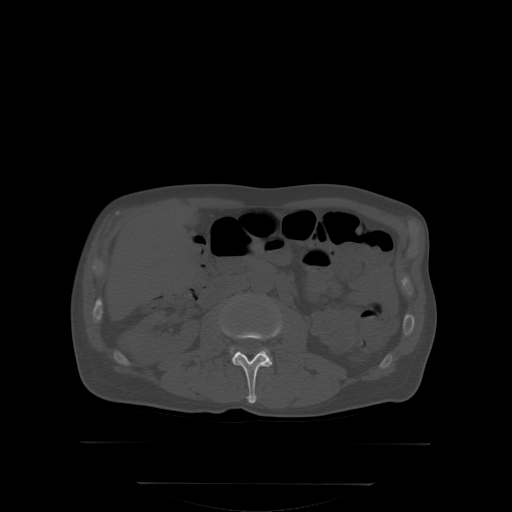
CT including the spine, one axial slice. Position 133 of 350 along the scan axis. Bone window (W 1800 / L 400 HU). 2.5 mm slice thickness. 512 × 512 image matrix, field of view 500 × 500 mm. Male patient, age 58 years. From the clinical record (not read from this slice): primary cancer: prostate; vertebrae with lytic lesions (as recorded): L1.
Outlined on this slice (semi-automatic segmentation, software-assisted and operator-edited):
- L2 vertebra: bounding box [x1, y1, x2, y2] px = [222, 320, 281, 403]
- L3 vertebra: [230, 349, 270, 364]